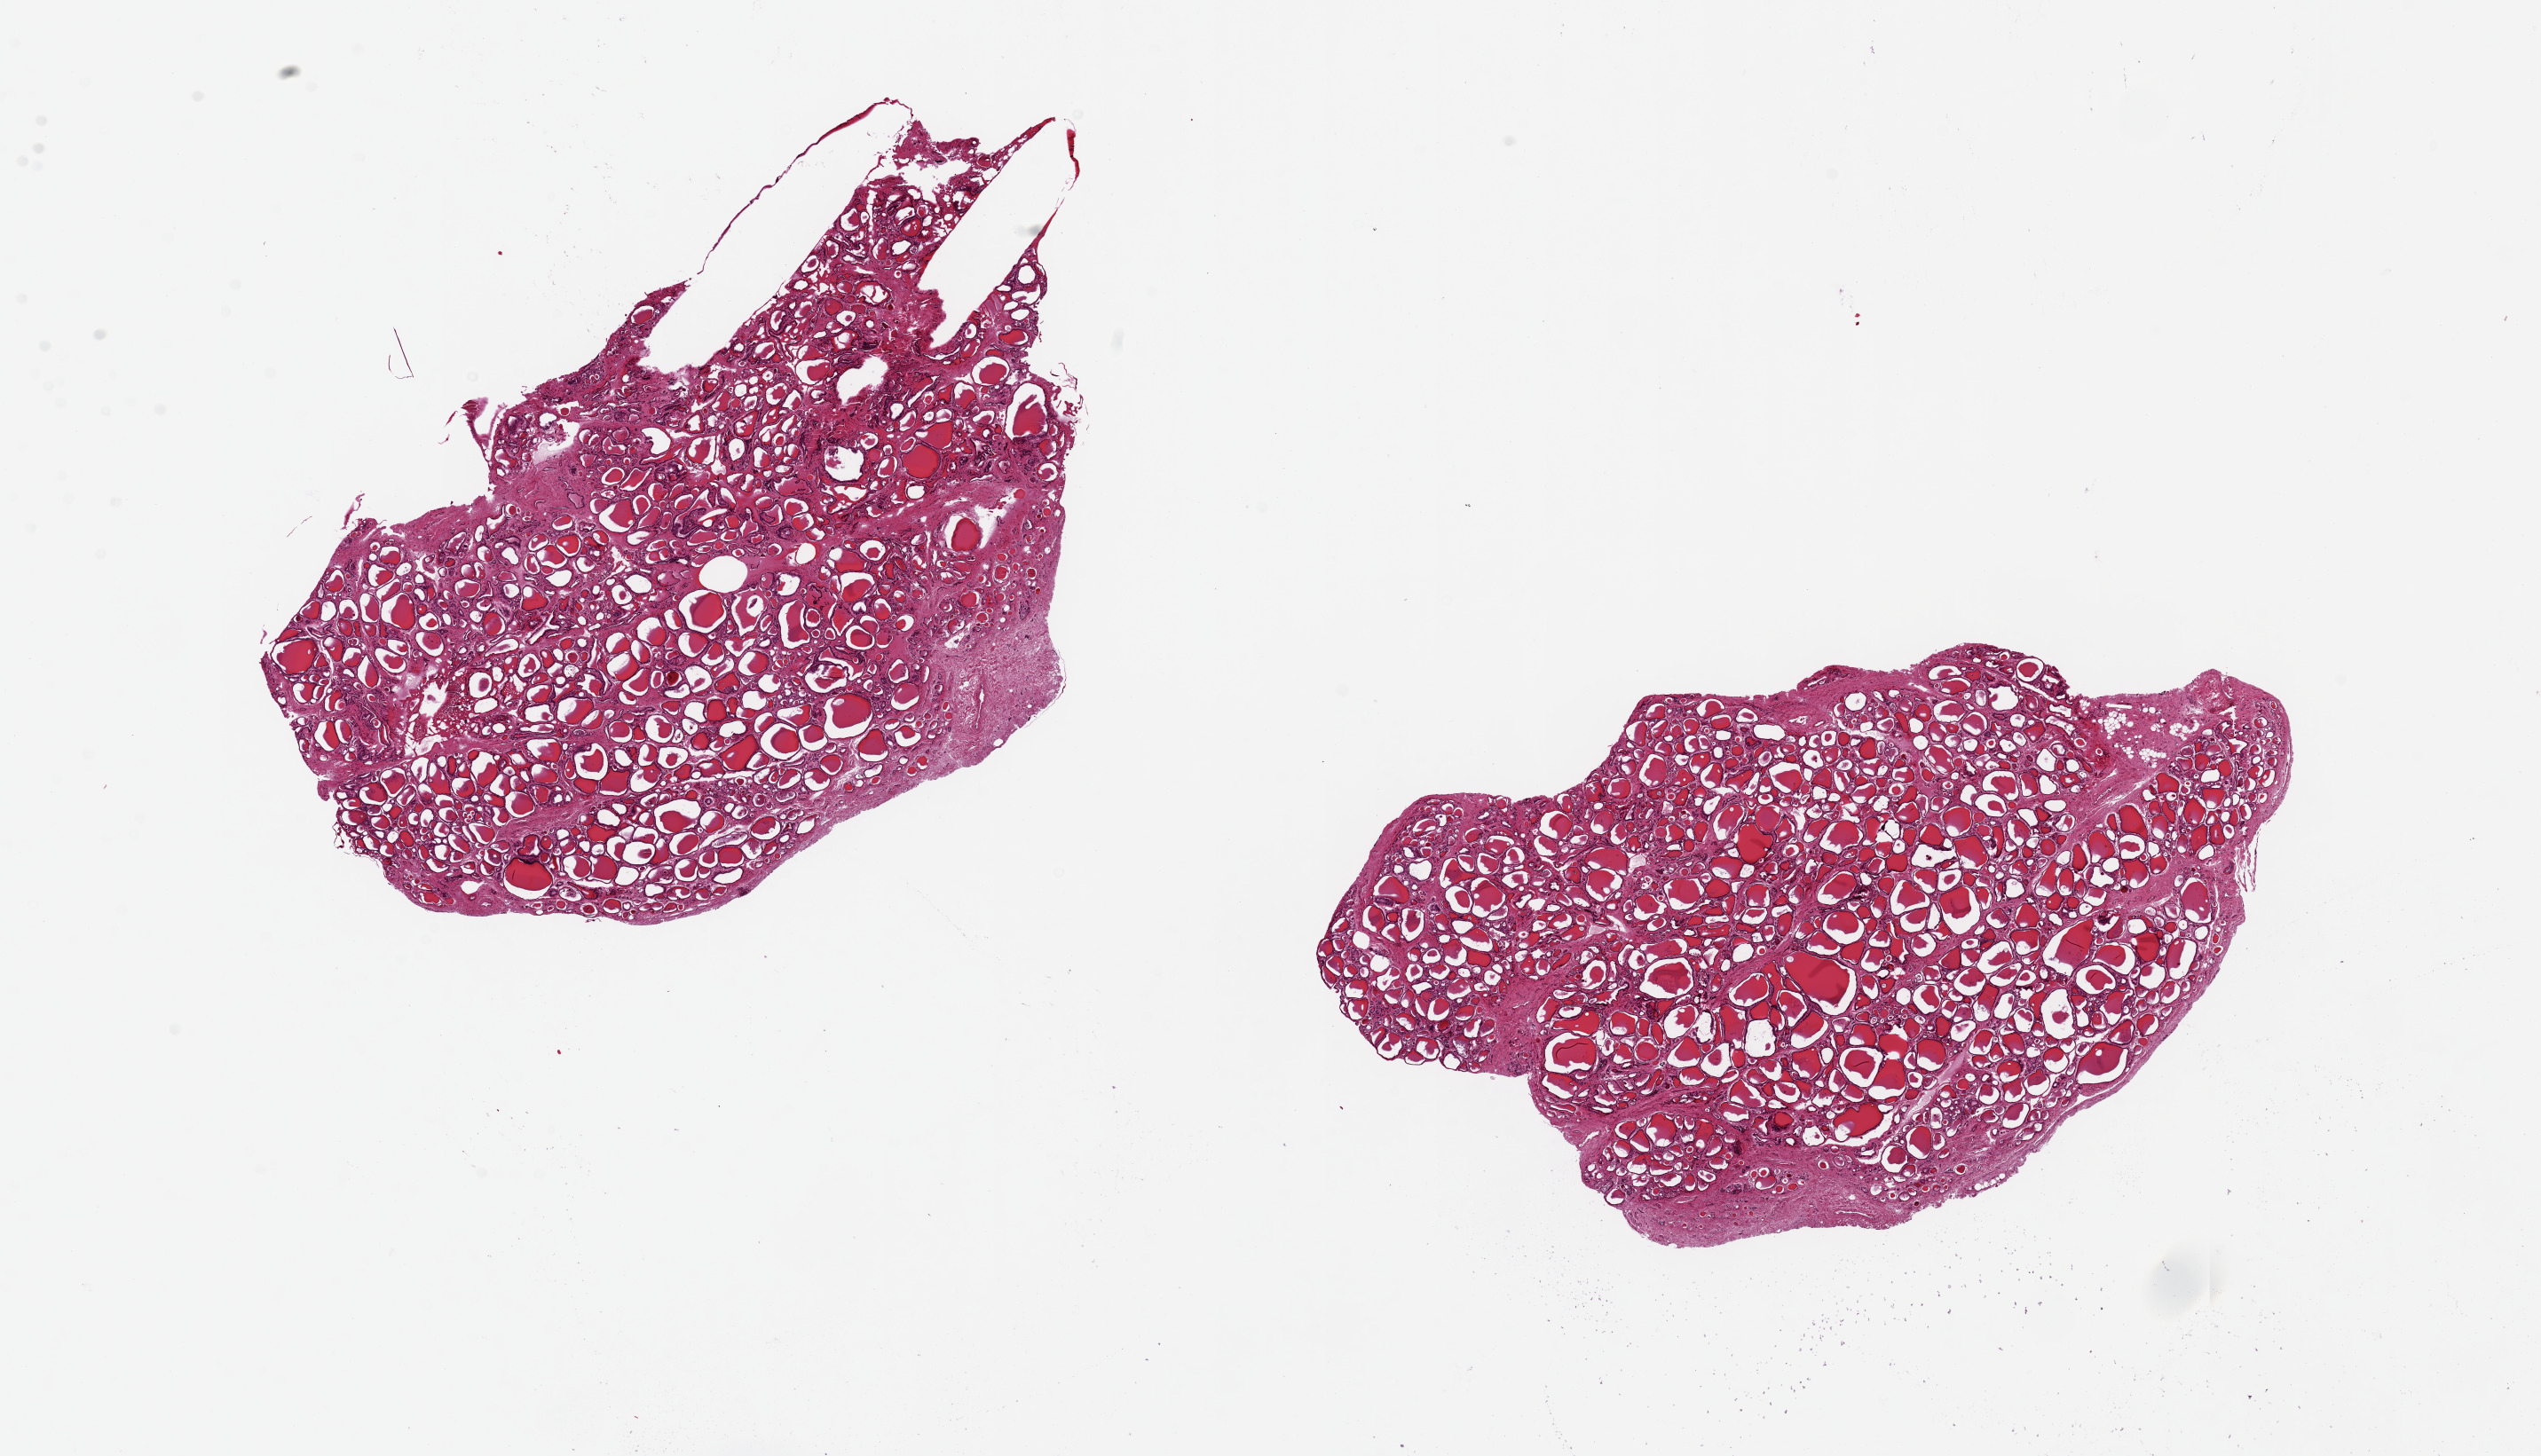
Digitized H&E-stained section — shown as a low-resolution overview of the whole scanned area (about 22.6 x 13.0 mm, from a 20x scan); PAXgene-fixed paraffin-embedded (PFPE) section; target tissue: thyroid; donor tissue sample. Donor: male.
- review note (as recorded): 2 pieces, 9x6 & 9x5.5mm; focal fibrosis